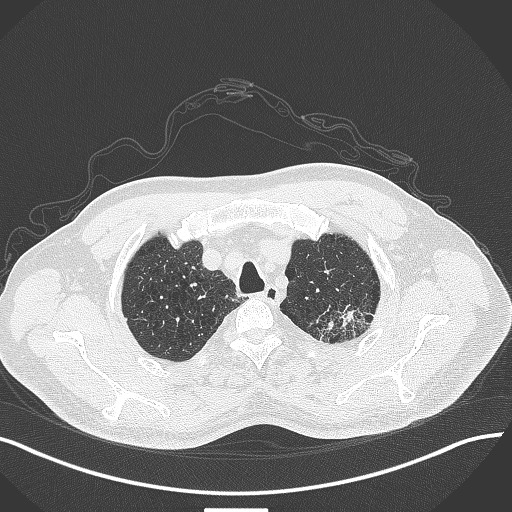
Chest CT, one axial slice; position 361 of 429 along the scan axis; lung window (W 1500 / L -600 HU); 1 mm slice thickness; 512 × 512 image matrix, field of view 400 × 400 mm. Patient: male, 55 years. Case-level facts recorded for this patient, not image findings: clinical TNM (as recorded): T3 N0 M1c.
Outlined on this slice (rectangle marked by the reading radiologist):
- lung tumour (recorded histology: adenocarcinoma): bounding box (x1, y1, x2, y2) in pixels: (310, 303, 373, 350)